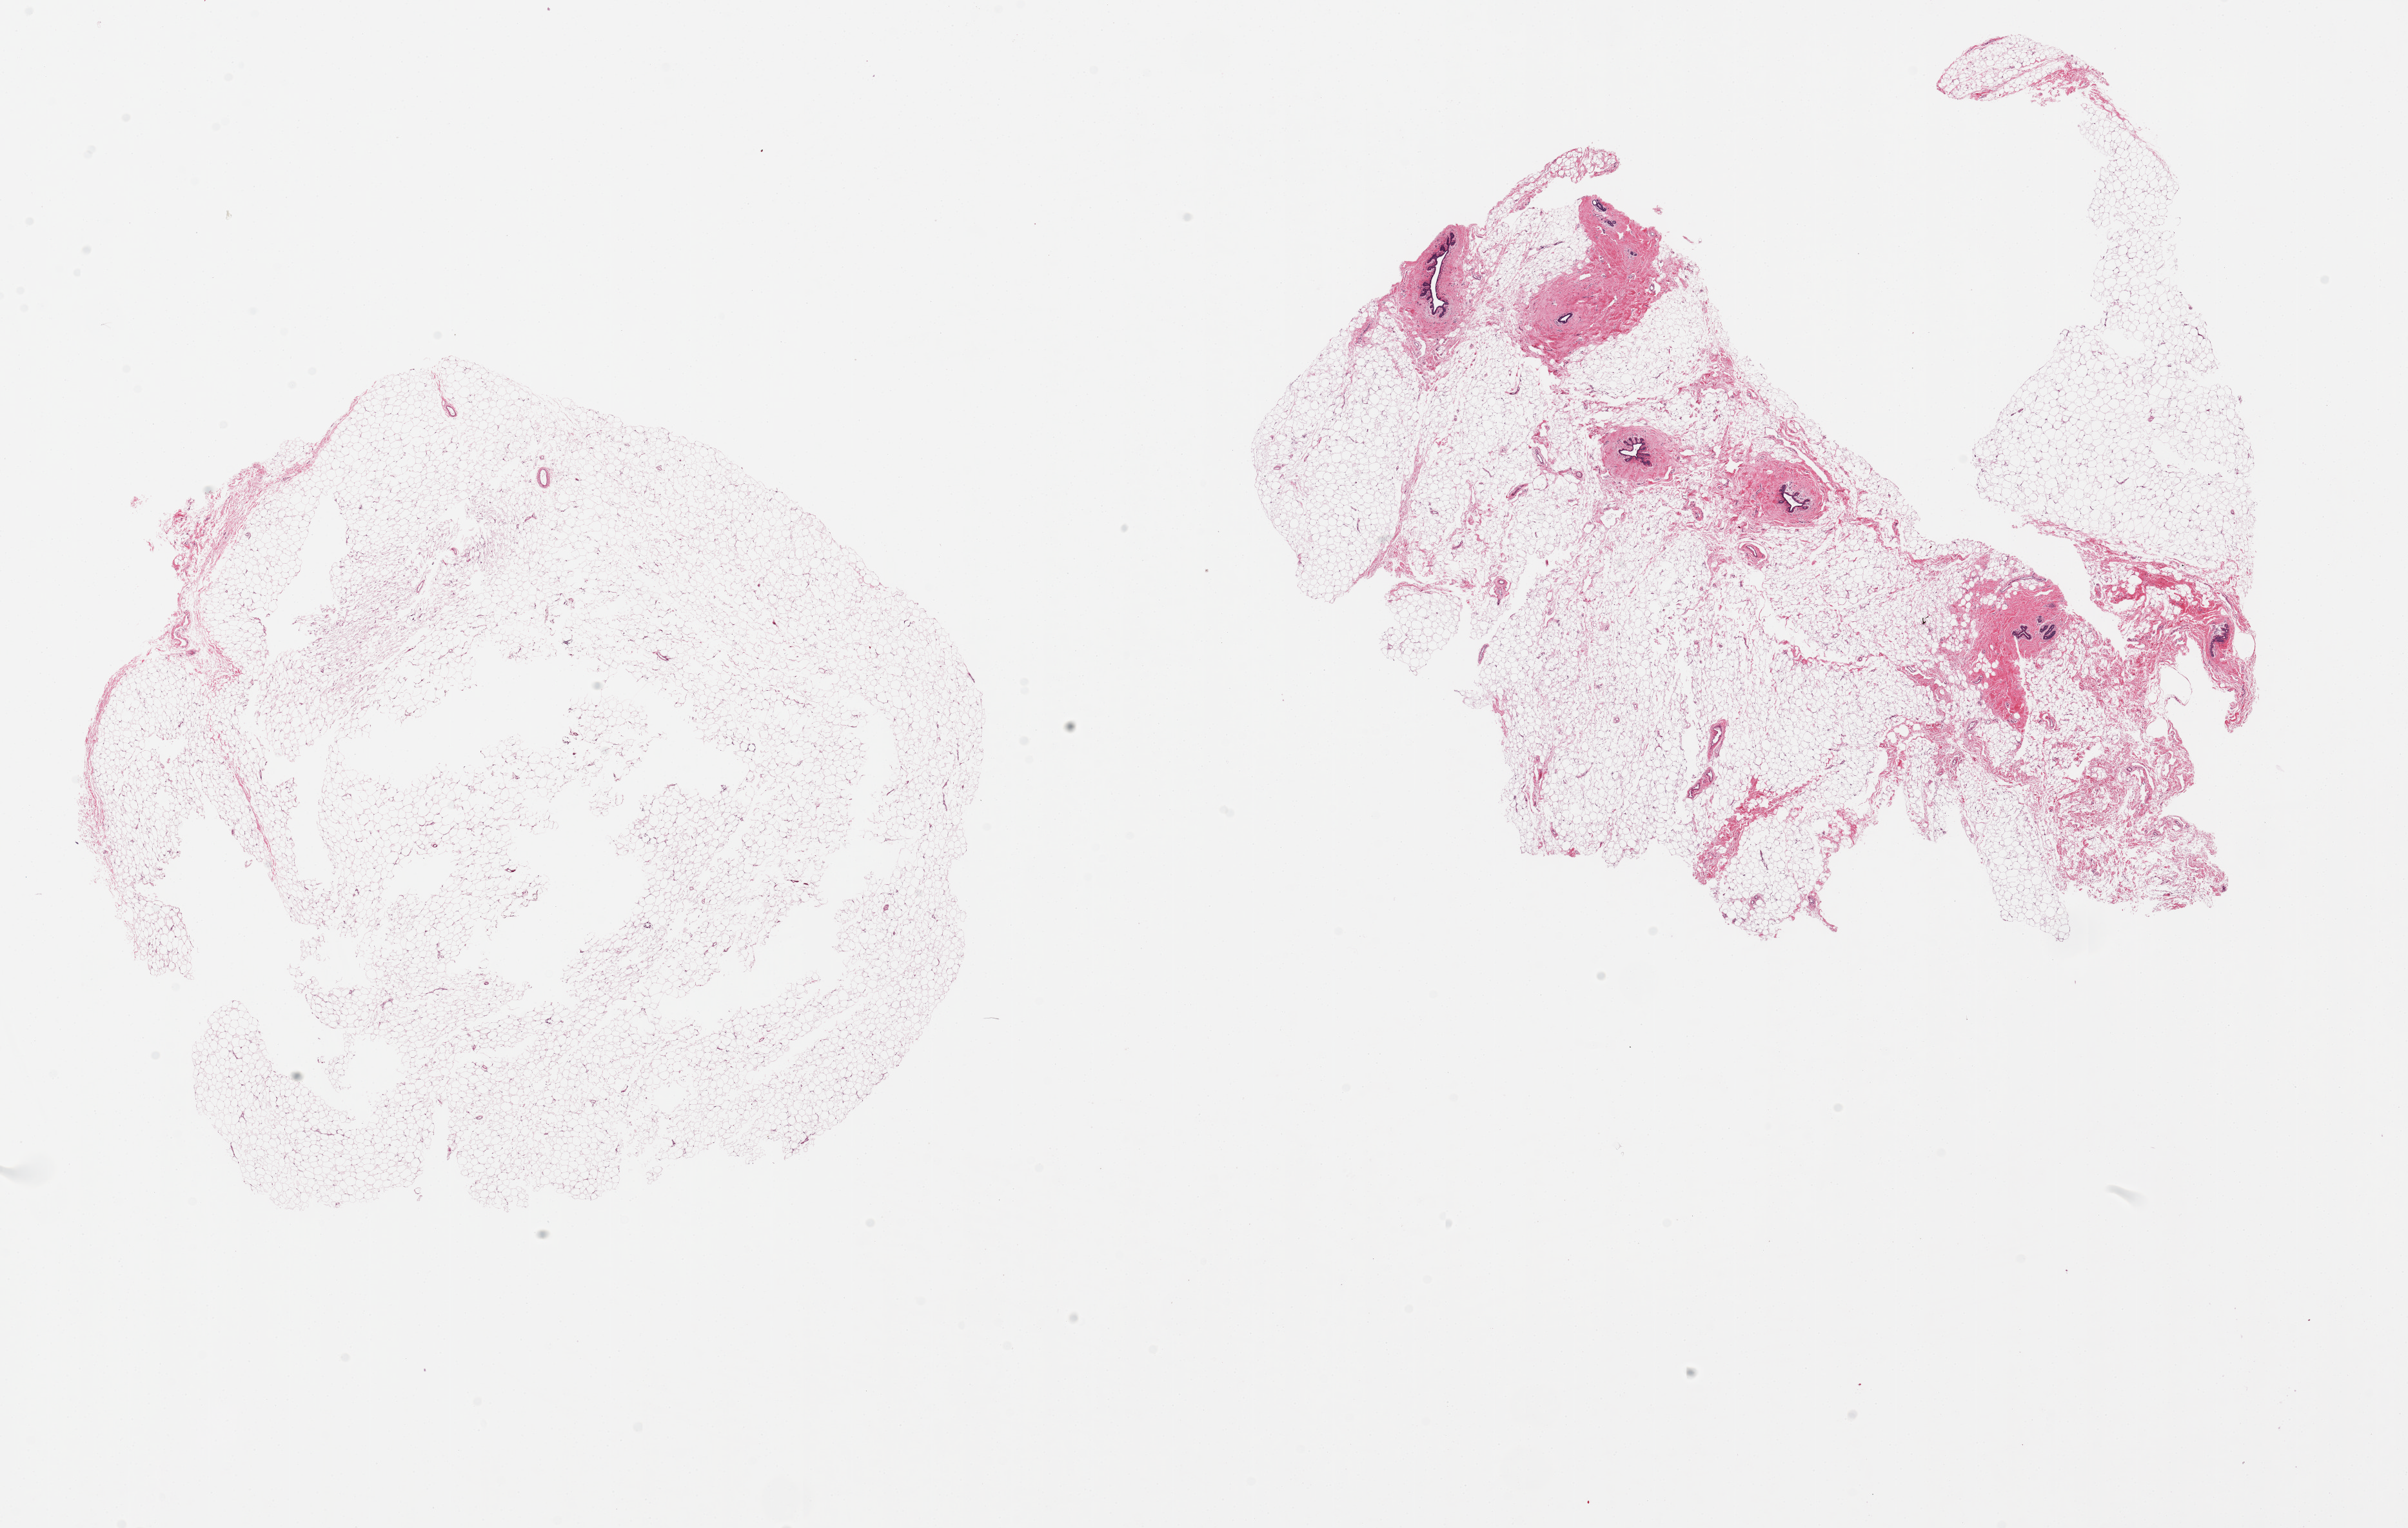
Whole-slide image, H&E stain, shown as a low-resolution overview of the whole scanned area (about 29.5 x 18.7 mm), PAXgene-fixed, paraffin-embedded tissue, section of breast (target tissue), donor tissue sample. Donor sex: female.
Reviewer comment on this tissue sample: 2 pieces, 12x11 & 13x12mm.